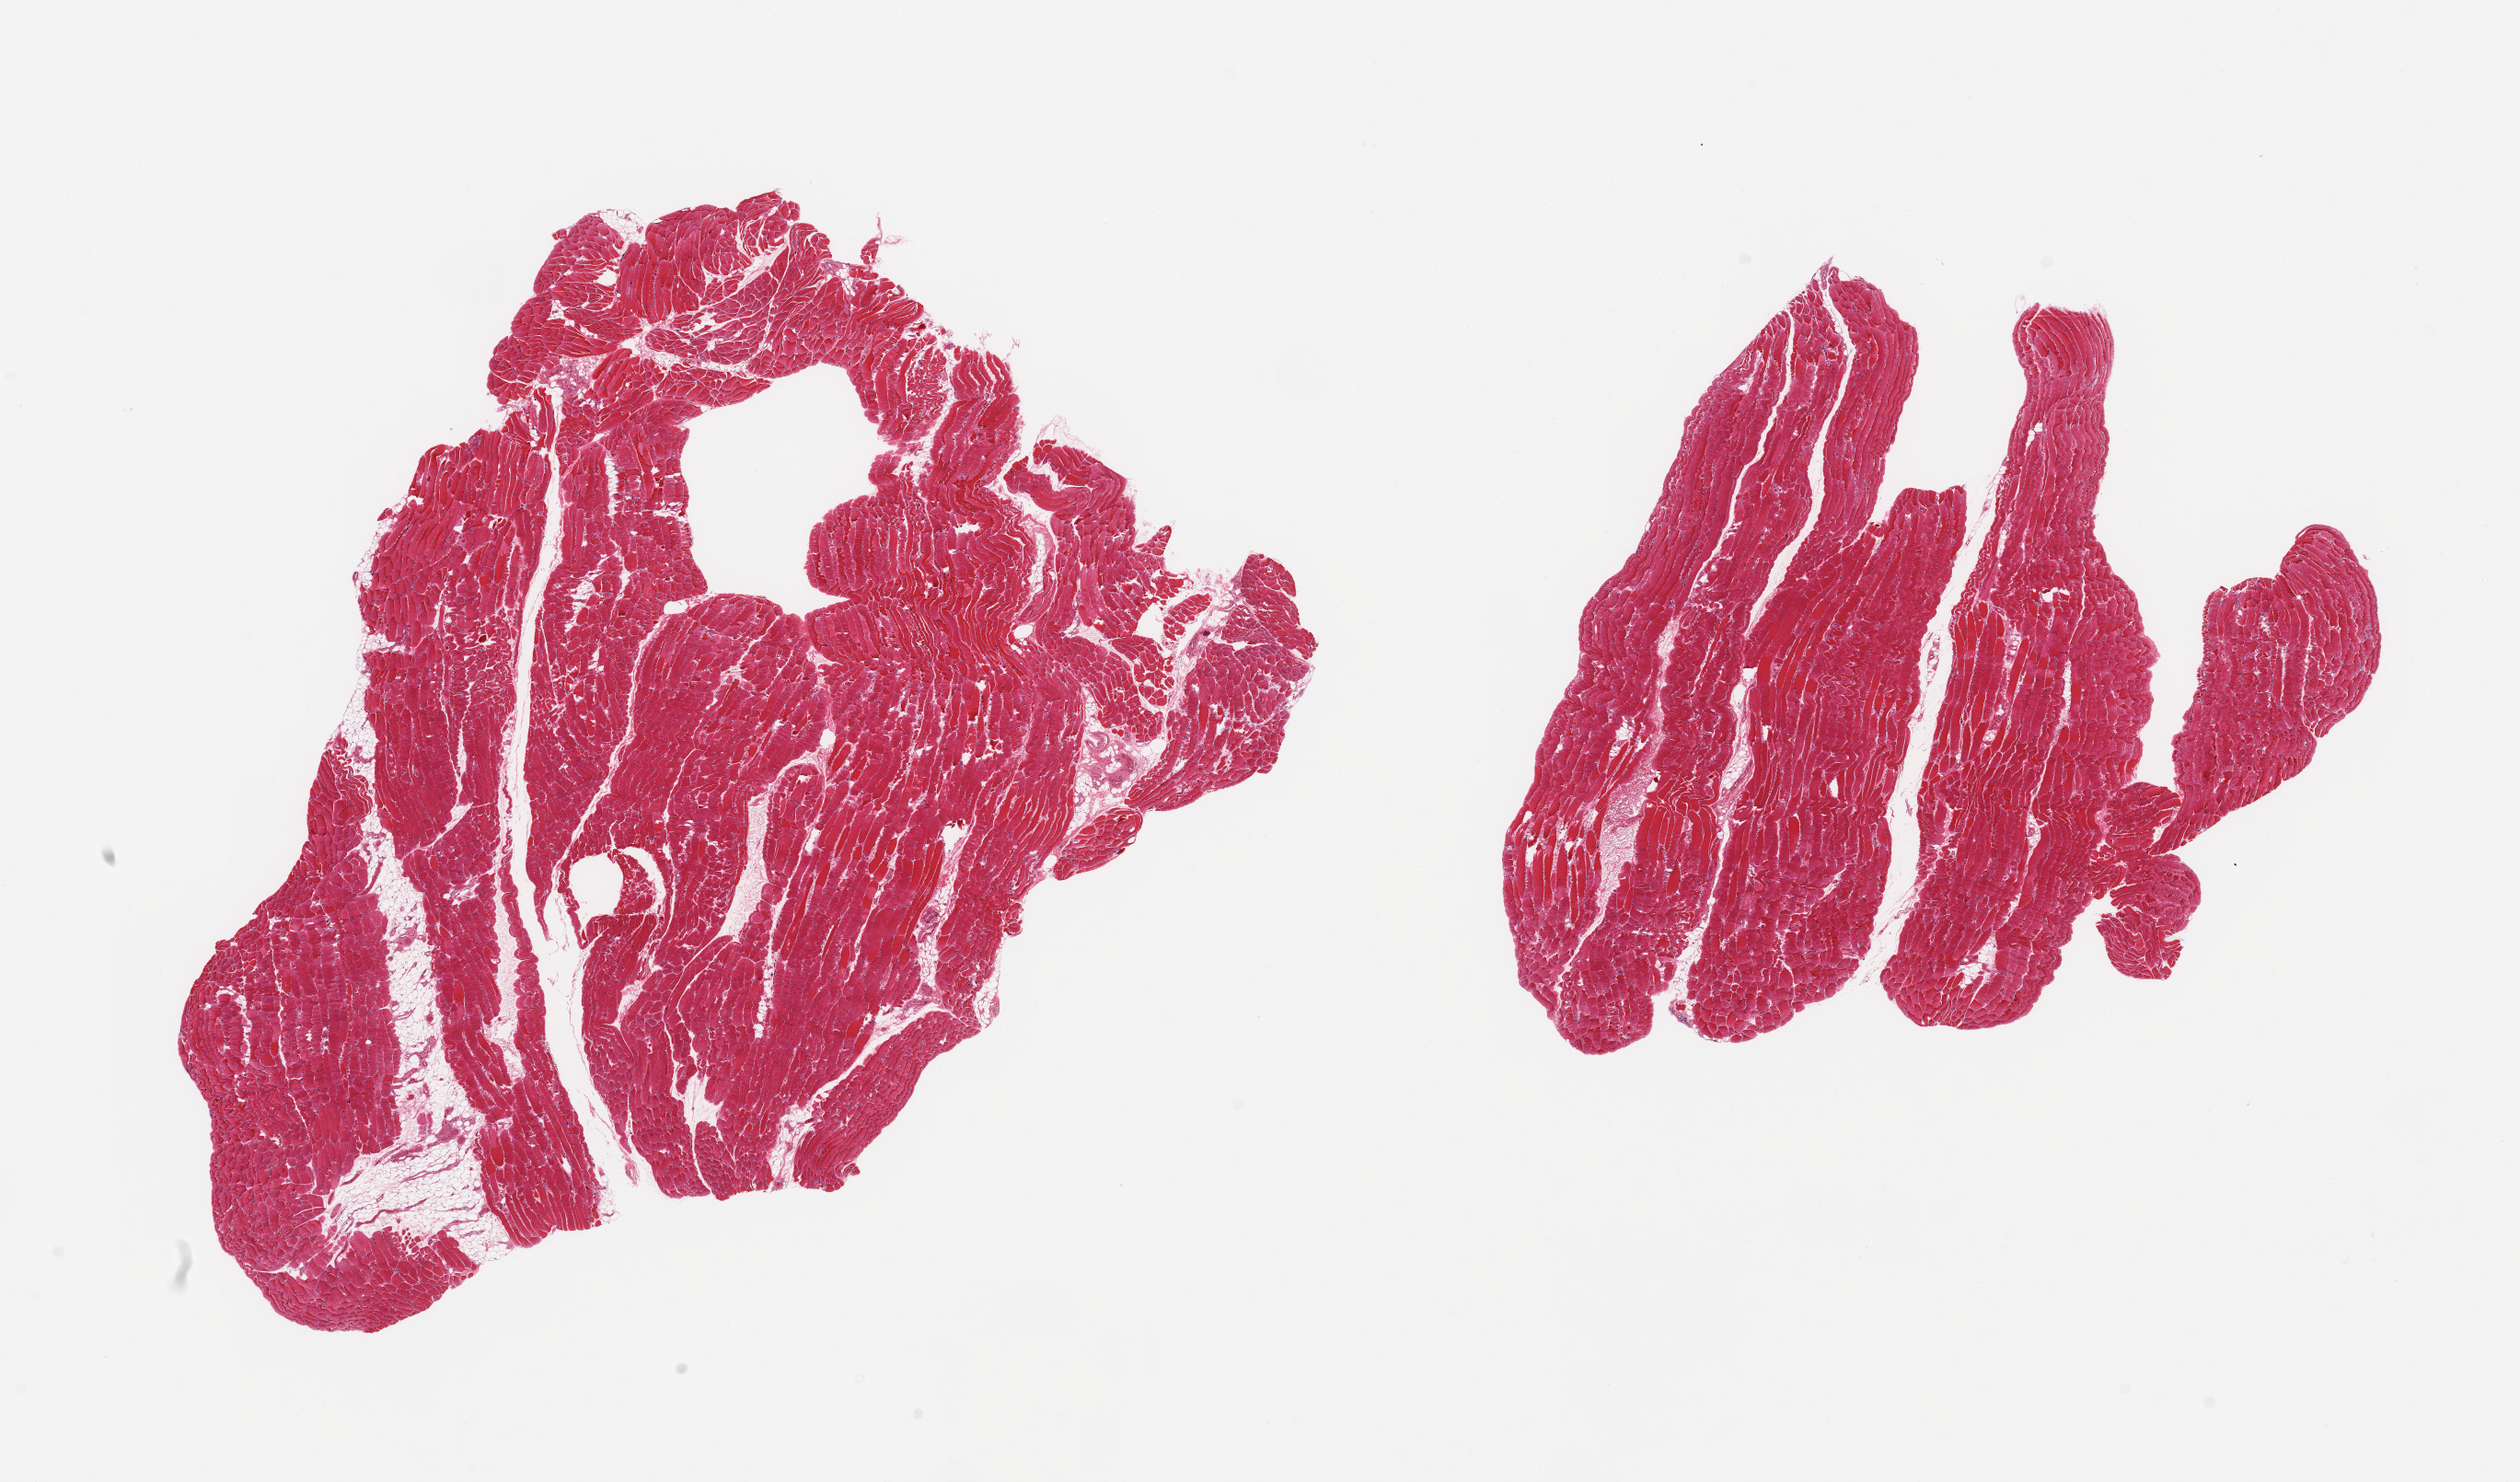
Digitized hematoxylin and eosin (H&E)-stained section — a low-resolution overview of the entire scanned area, about 21.7 x 12.7 mm (from a 20x scan). PAXgene-fixed paraffin-embedded (PFPE) section. Target tissue: skeletal muscle. Tissue donor sample. Male donor.
- reviewer comment on this tissue sample: 2 pieces; 5% internal fat